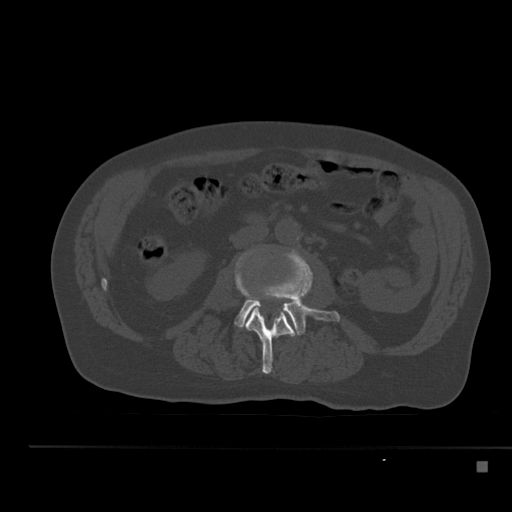
CT including the spine, one axial slice; slice 174 of 517 in the series (ordered by position); 120 kVp; bone window (W 1800 / L 400 HU); 512 × 512 image matrix, field of view 408 × 408 mm. Patient: male, 70 years. Case-level facts recorded for this patient, not image findings: primary cancer: renal; vertebrae with lytic lesions (as recorded): T4, T6, T10, T12, L3, L4, L5.
Outlined on this slice (semi-automatic segmentation, software-assisted and operator-edited):
- L2 vertebra: bounding box (x1, y1, x2, y2) in pixels: (235, 265, 295, 374)
- L3 vertebra: (235, 250, 340, 336)